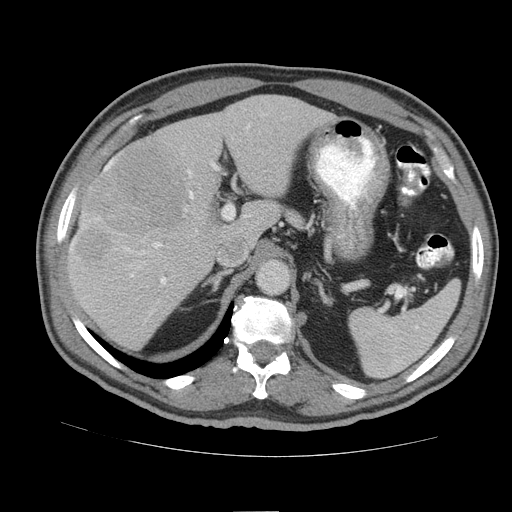
Contrast-enhanced abdominal CT (liver protocol), one axial slice; position 59 of 105 along the scan axis; reconstruction kernel STANDARD; soft-tissue window (W 400 / L 40 HU); 512 × 512 image matrix. Case-level facts recorded for this patient, not image findings: diagnosis: hepatocellular carcinoma (patient treated with transarterial chemoembolisation; whether this scan precedes or follows treatment is not stated here); TNM stage (as recorded): Stage-IIIB; Child-Pugh class: A; tumour nodularity: multinodular.
Structures marked on this image (semi-automatically segmented with operator editing):
- liver parenchyma outside the tumour (the mass and vessels are separate outlines, so this box may not span the whole liver): bounding box <68,94,336,348> (left, top, right, bottom; pixels)
- mass: <77,145,182,262>
- liver vessels: <71,126,249,284>